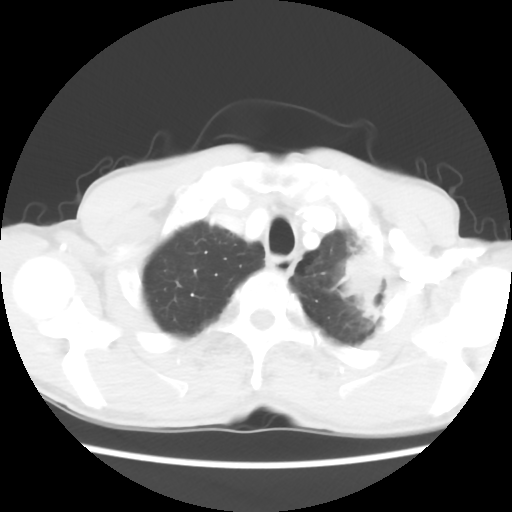
Chest CT, one axial slice; position 53 of 60 along the scan axis; 120 kVp; lung window (W 1500 / L -600 HU); 5 mm slice thickness; 512 × 512 image matrix, field of view 308 × 308 mm. Male patient, age 64 years. From the clinical record (not read from this slice): clinical TNM (as recorded): T3 N3 M0; histopathological grade: G3.
Annotated regions visible in this slice (rectangle marked by the reading radiologist):
- lung tumour (recorded histology: adenocarcinoma): bounding box [x1, y1, x2, y2] px = [337, 248, 391, 333]